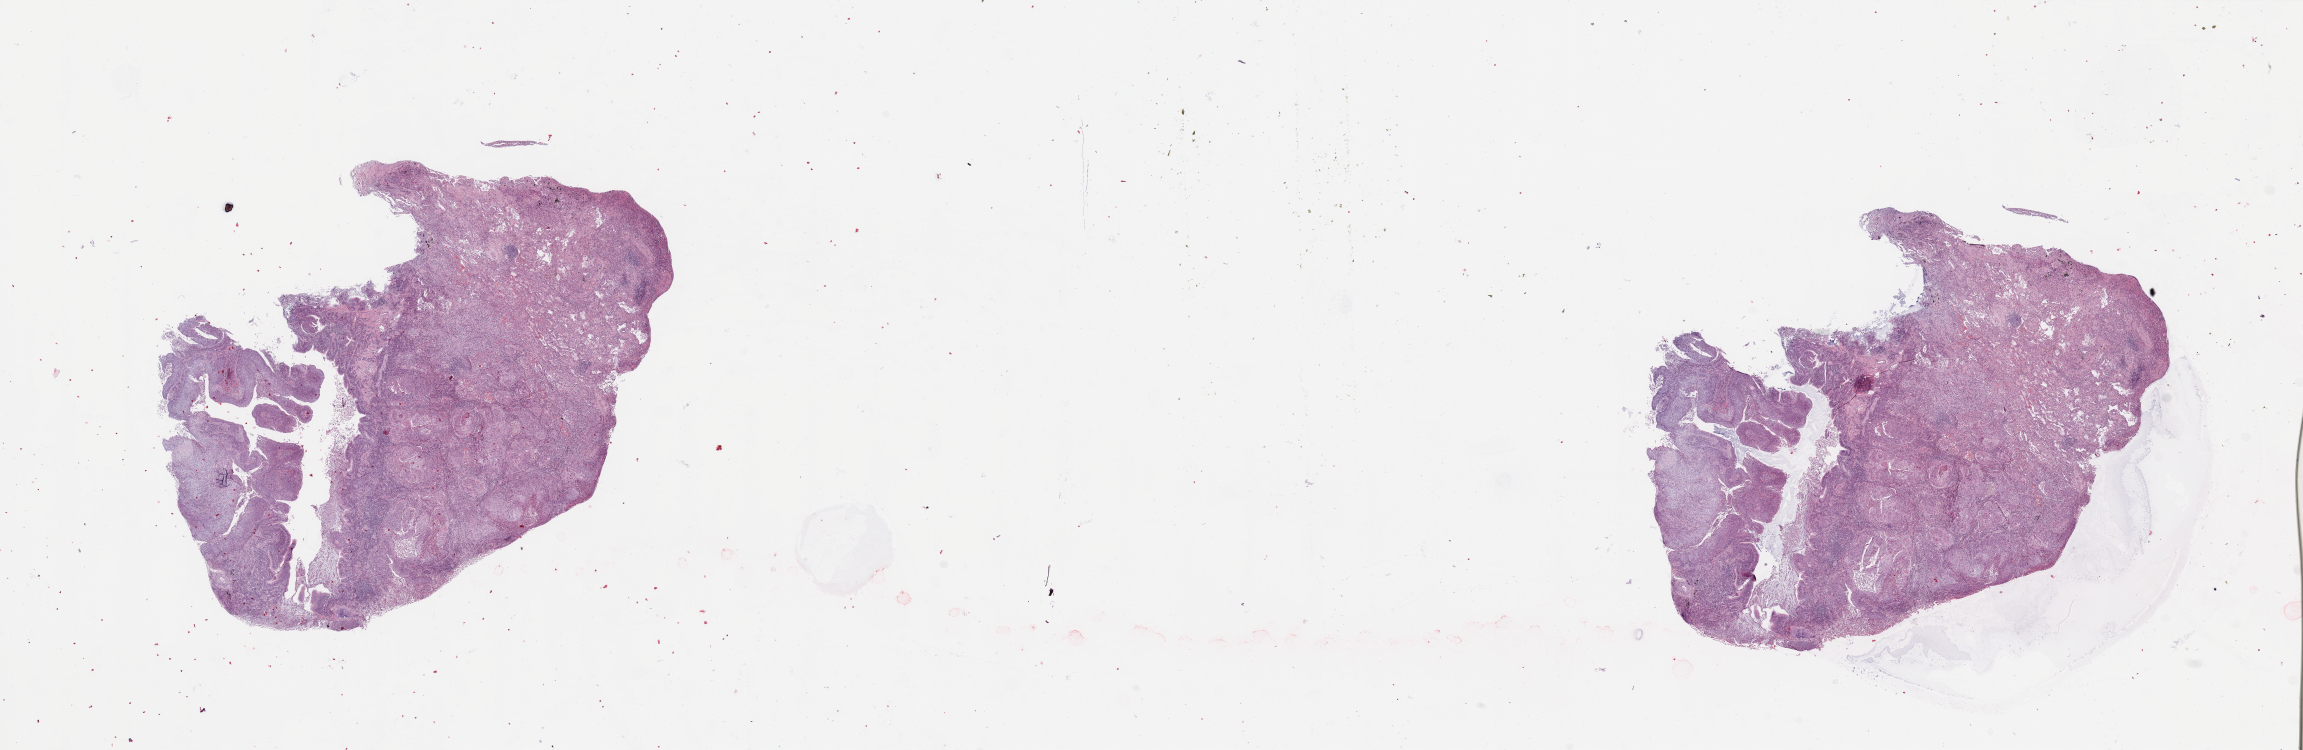
Hematoxylin and eosin (H&E) stained whole-slide image, a low-resolution overview of the entire scanned area, about 36.4 x 11.9 mm; tumour tissue sample, lung. Patient: male, age 53 years. Histologic grade: G2 (moderately differentiated).
Histologic diagnosis: Squamous cell carcinoma, NOS. AJCC pathologic stage: IIIA.